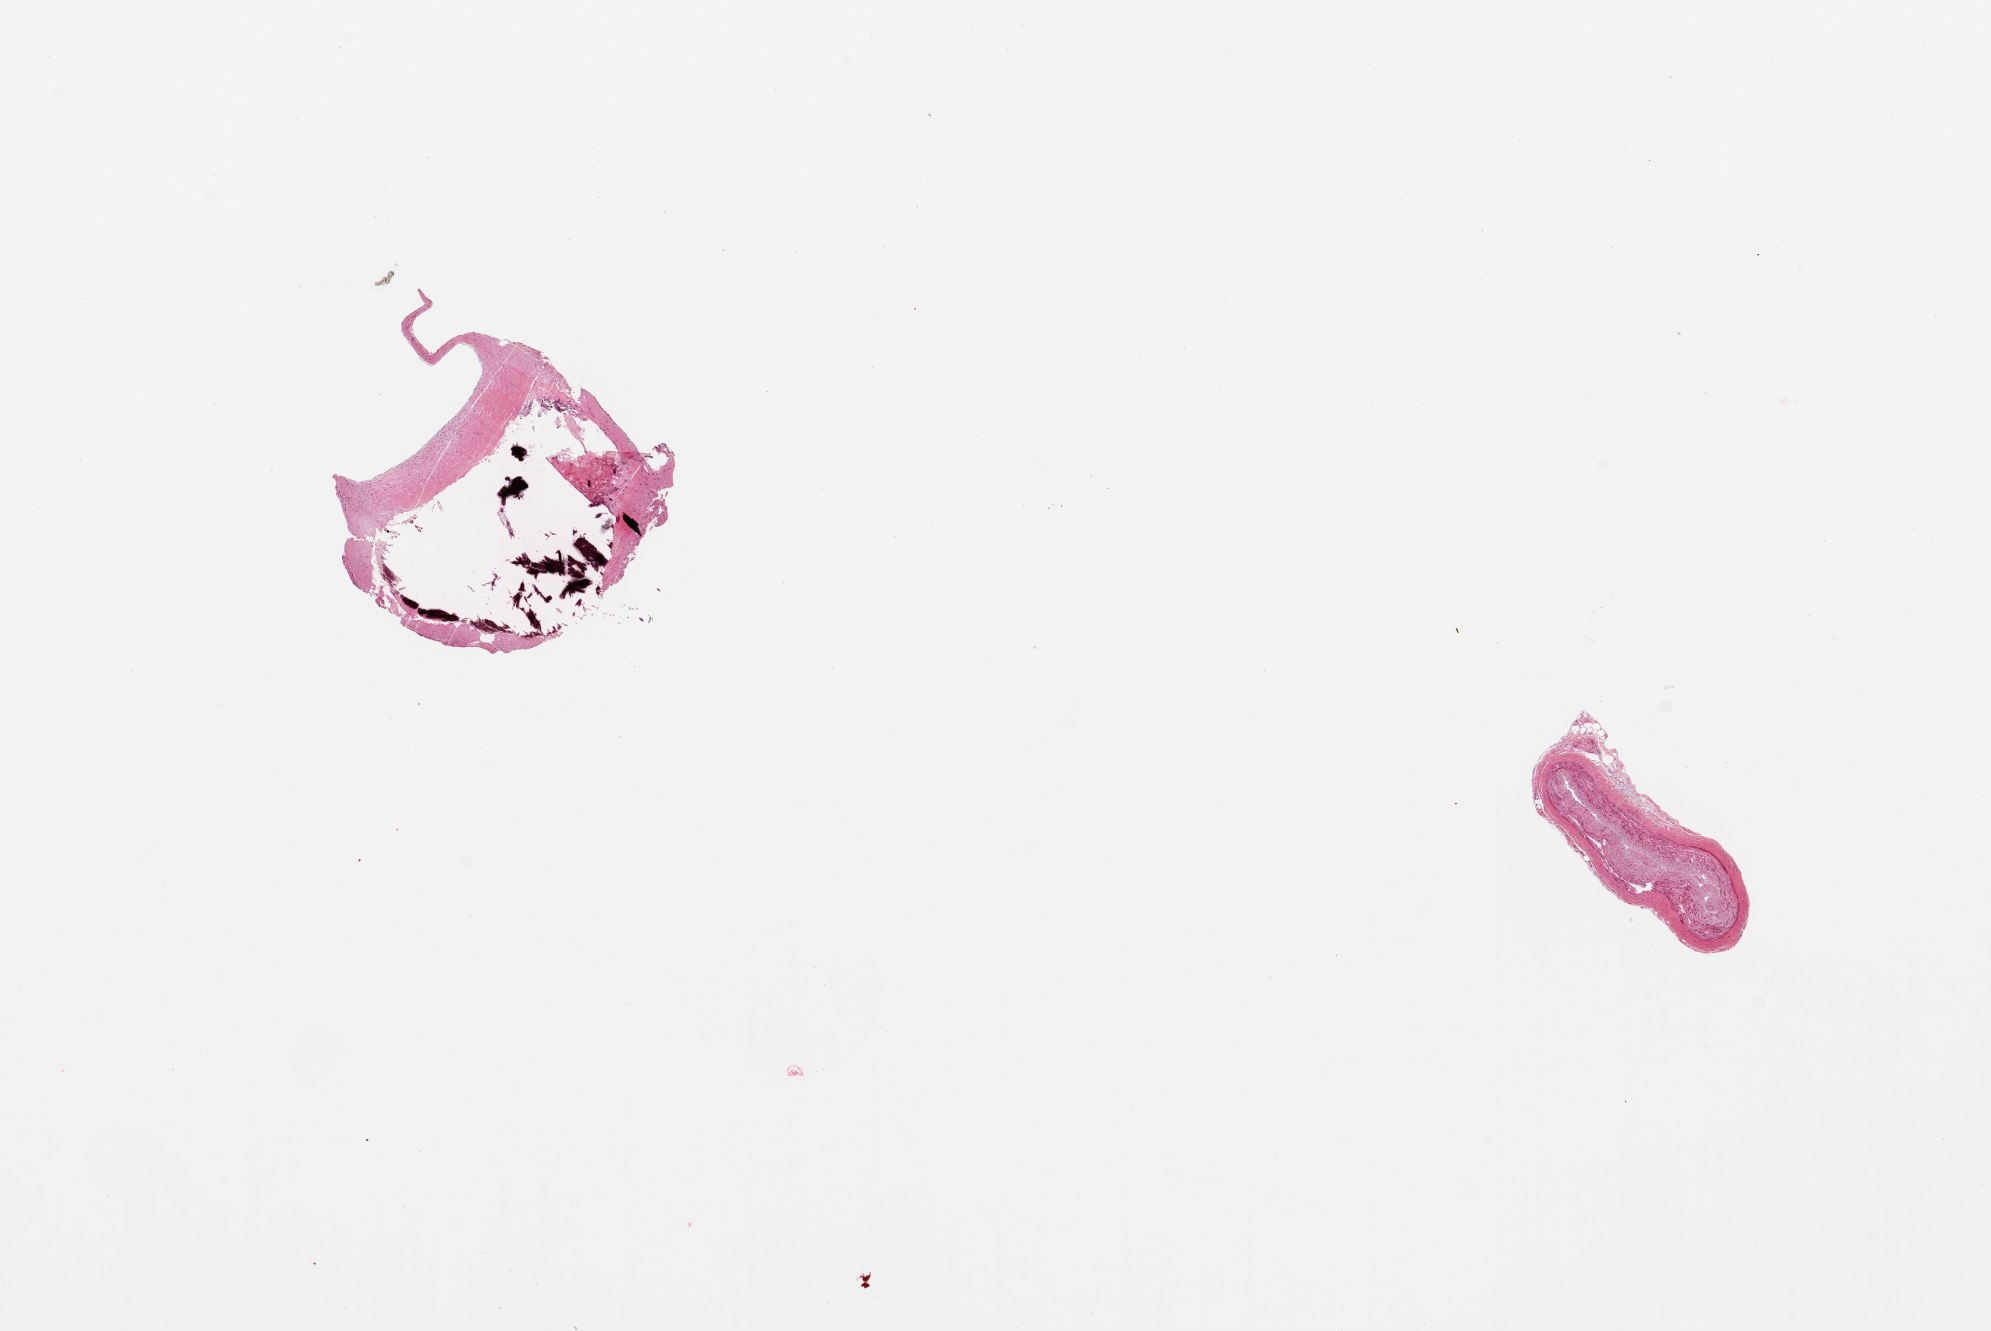
Haematoxylin and eosin whole-slide image, brightfield — shown as a low-resolution overview of the whole scanned area (about 15.8 x 10.5 mm). PAXgene-fixed paraffin-embedded (PFPE) section. Sampled site (target tissue): coronary artery. Tissue donor sample. Male donor.
Pathologist's review note for this sample: 2 pieces; 1 with large [2mm] calcified plaque.